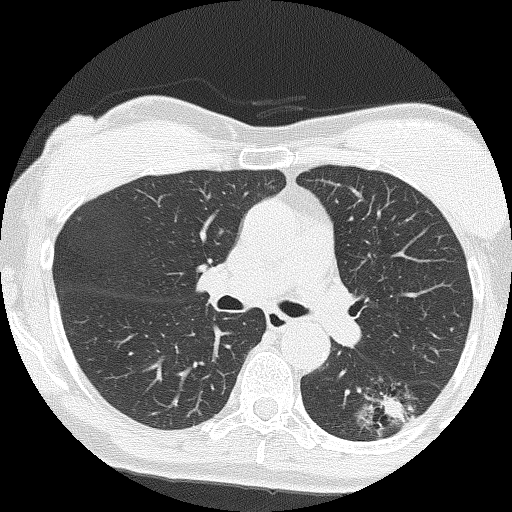
Low-dose screening chest CT, axial slice; second annual screen; lung window (W 1500 / L -600 HU); lung (sharp) reconstruction kernel (FC51). Female, age 64 years at enrolment. Former smoker at enrolment.
• Expert reader's lesion annotation, bounding box <356,377,431,439> (left, top, right, bottom; pixels).
• The screening reader recorded 3 non-calcified nodules or masses ≥4 mm on this exam (right upper lobe, right upper lobe, right middle lobe); which of them this box marks is not recorded.
• Participant outcome: lung cancer diagnosed 576 days after this screen (after the third annual screen) — adenocarcinoma, NOS, left lower lobe, moderately differentiated (G2), stage IA (AJCC 6th edition), 17 mm at pathology.